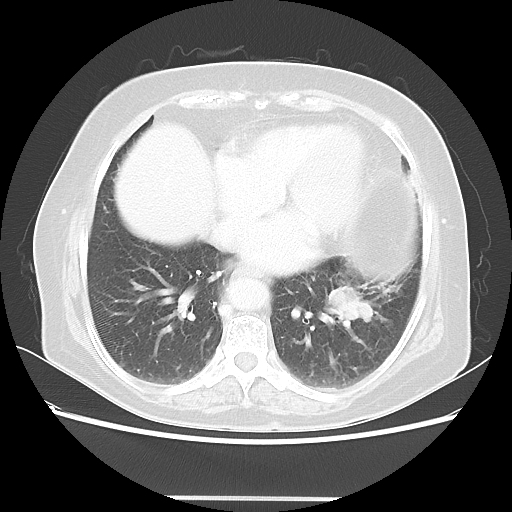
Chest CT, one axial slice. Slice 21 of 56 in the series (ordered by position). Lung window (W 1500 / L -600 HU). 5 mm slice thickness. 512 × 512 image matrix, field of view 360 × 360 mm. Female patient, age 73 years. Case-level facts recorded for this patient, not image findings: clinical TNM (as recorded): T1c N0 M0.
Annotated regions visible in this slice (rectangle marked by the reading radiologist):
- lung tumour (recorded histology: adenocarcinoma): box from (x=322, y=283) to (x=381, y=338) px